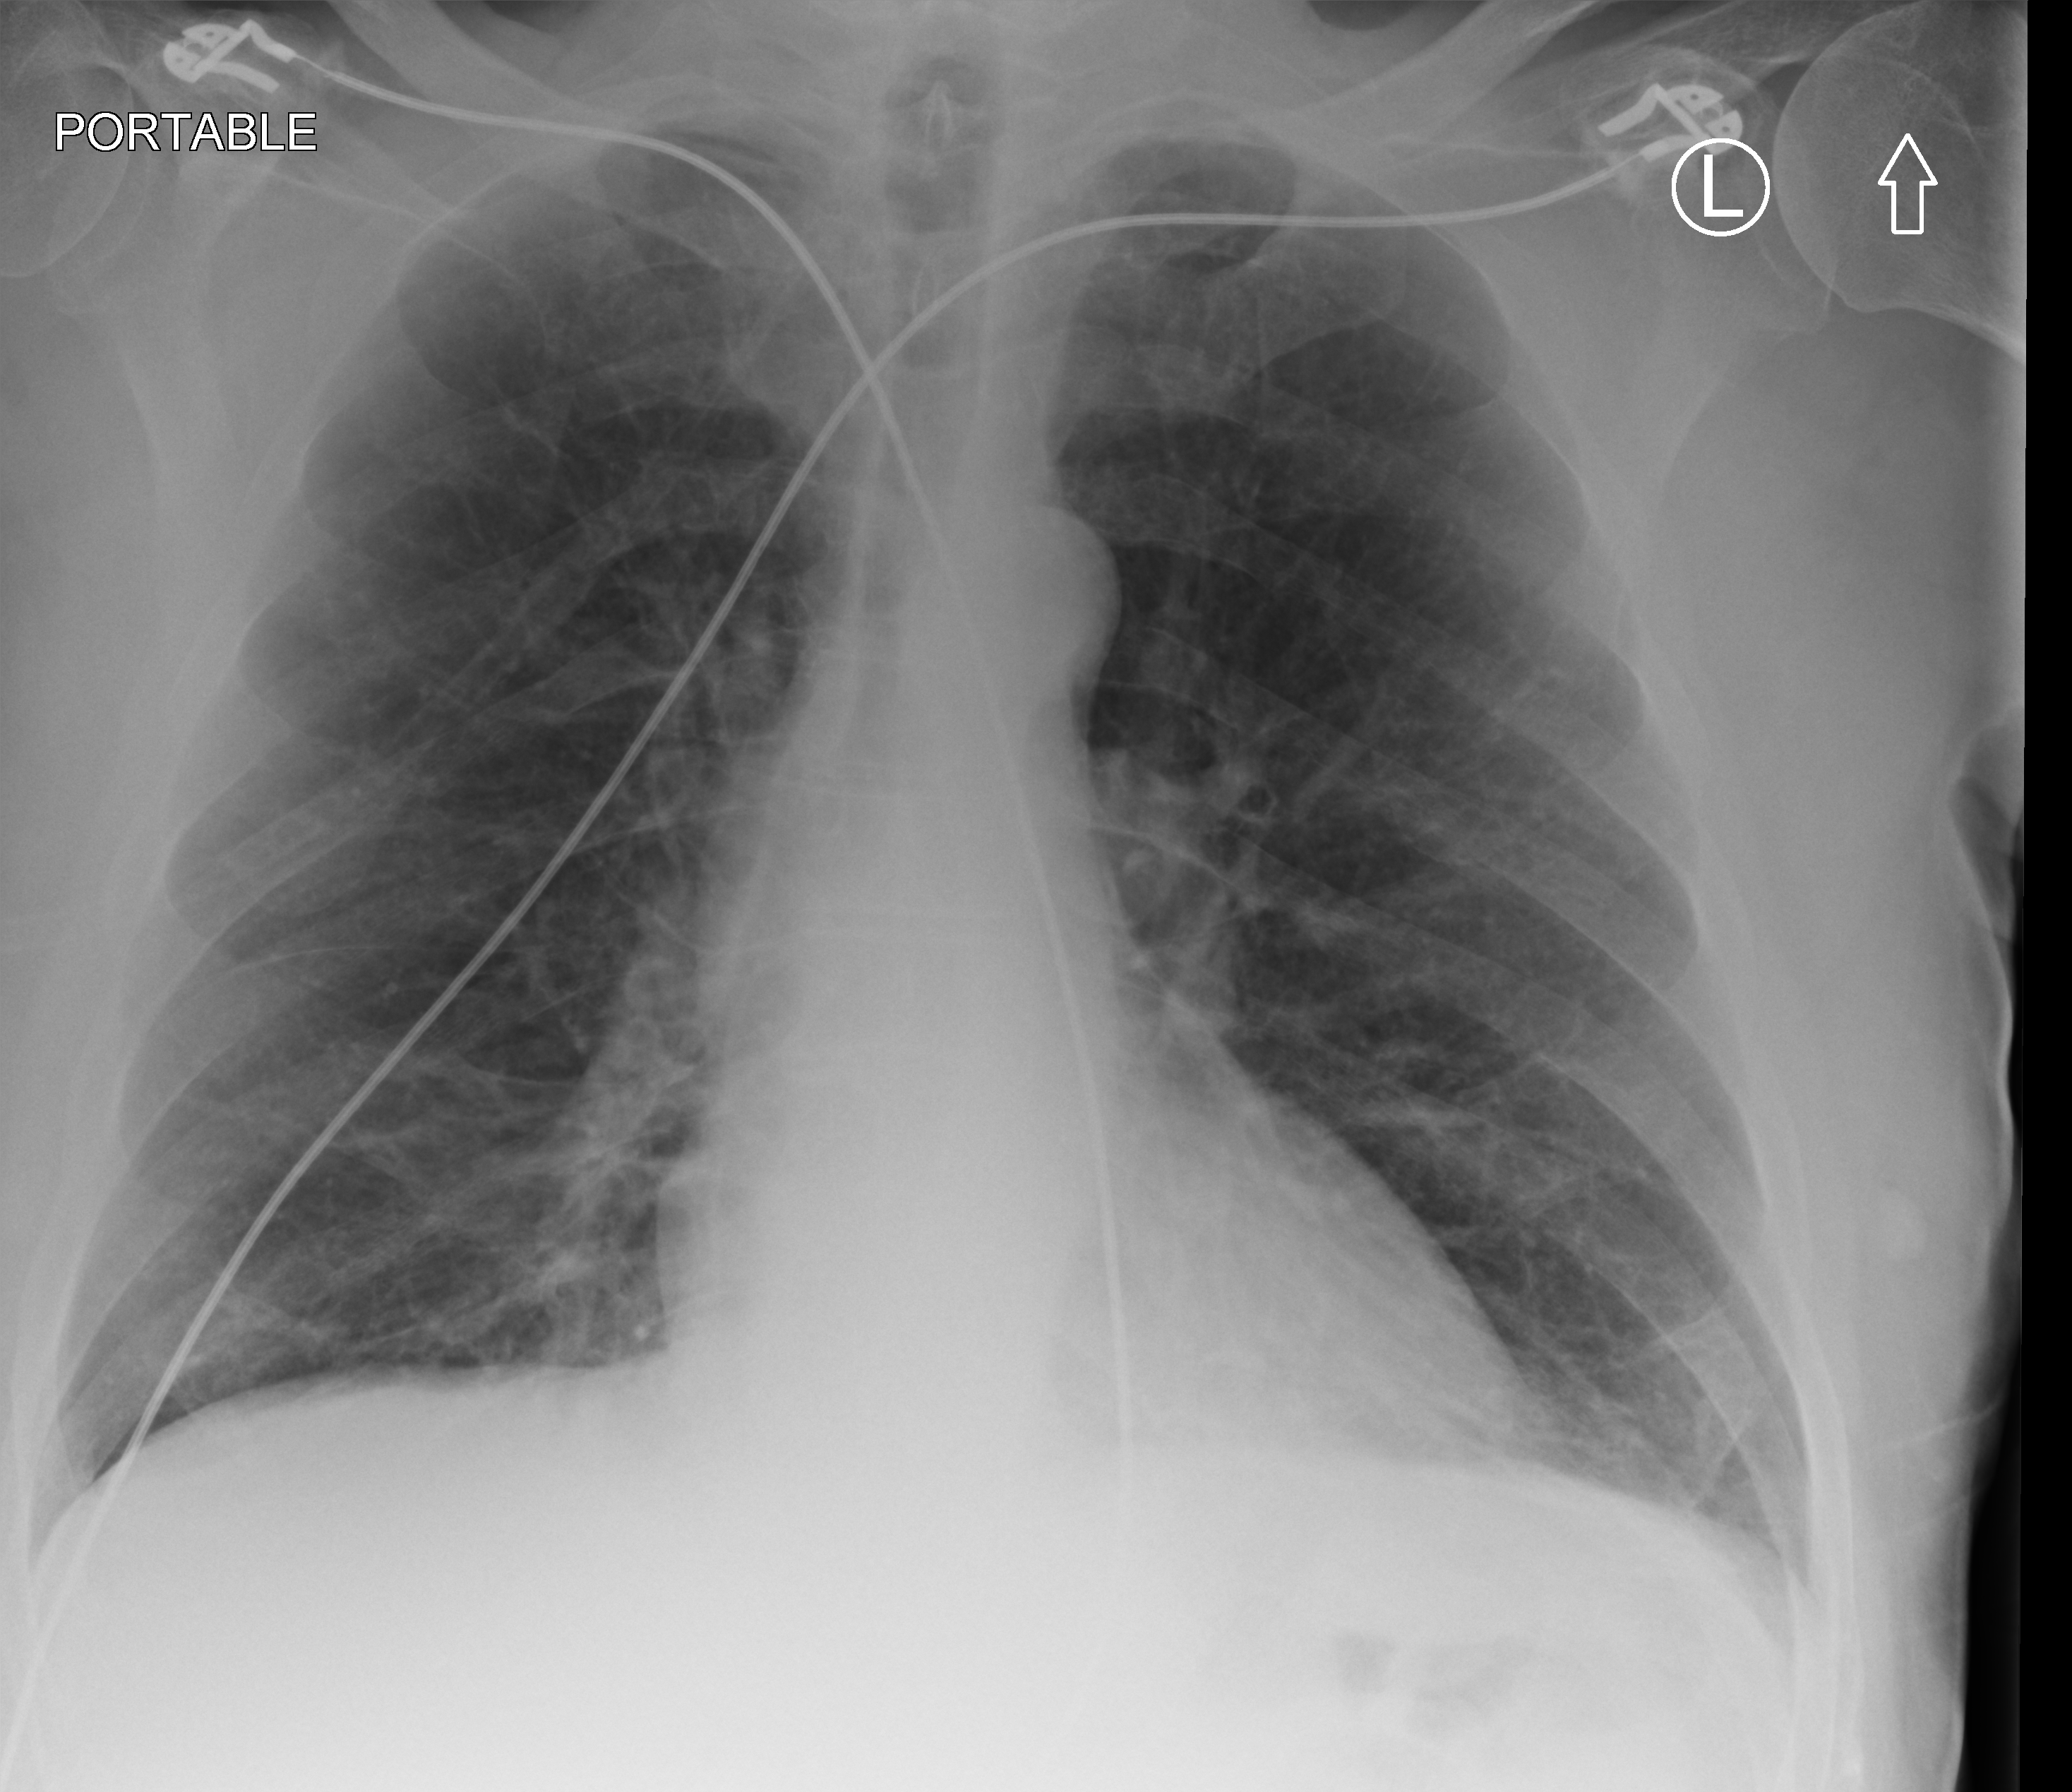
Chest X-ray (portable); anteroposterior (AP) projection. Patient hospitalised with COVID-19; male, aged 60–74 years.
From the hospital-stay record, not from the radiograph (when in the stay this image was taken is not recorded): hypertension (admission record): no.